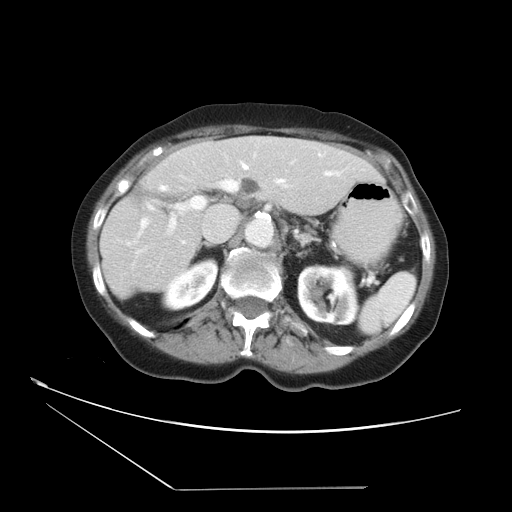
Contrast-enhanced abdominal CT, one axial slice. Position 21 of 36 along the scan axis. Intravenous contrast given. Soft-tissue window (W 400 / L 40 HU). 5 mm slice thickness. 512 × 512 image matrix, field of view 384 × 384 mm. Female patient, age 81 years. Case-level facts recorded for this patient, not image findings: diagnosis: colorectal cancer liver metastases, imaged before liver resection; multiple liver metastases: no; largest metastasis: 1.6 cm; disease in both lobes: no.
Annotated regions visible in this slice (expert manual segmentation):
- hepatic veins: box from (x=128, y=164) to (x=330, y=245) px
- liver: (x=101, y=137)–(x=382, y=297)
- planned liver remnant (the part of the liver to remain after resection): (x=100, y=139)–(x=382, y=297)
- portal vein (with intrahepatic branches): (x=136, y=178)–(x=237, y=256)
- liver metastasis: (x=240, y=176)–(x=262, y=195)